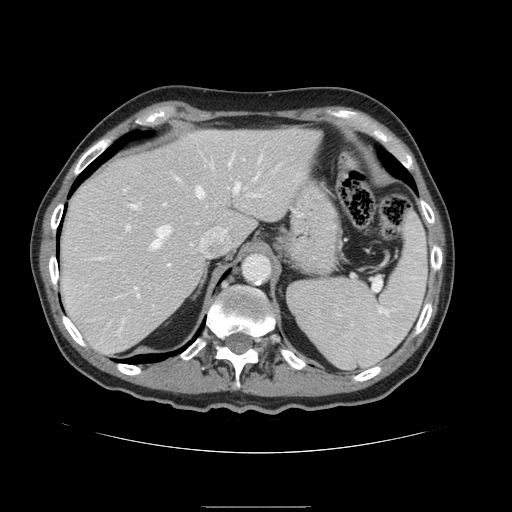
Contrast-enhanced abdominal CT, one axial slice; position 114 of 168 along the scan axis; intravenous contrast given; soft-tissue window (W 400 / L 40 HU); 2.5 mm slice thickness; 512 × 512 image matrix, field of view 386 × 386 mm. Male patient, age 74 years. Case-level facts recorded for this patient, not image findings: diagnosis: colorectal cancer liver metastases, imaged before liver resection; multiple liver metastases: no; largest metastasis: 14.5 cm; disease in both lobes: yes.
Outlined on this slice (outlined manually by an expert reader):
- hepatic veins: bounding box [x1, y1, x2, y2] px = [132, 157, 262, 247]
- liver: [60, 128, 321, 355]
- planned liver remnant (the part of the liver to remain after resection): [60, 128, 321, 354]
- portal vein (with intrahepatic branches): [120, 194, 260, 298]